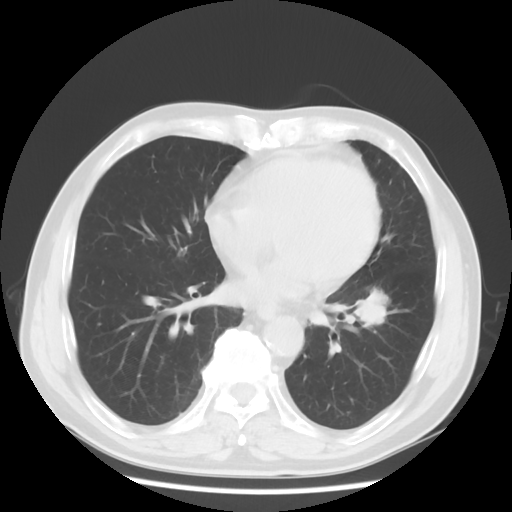
Chest CT, one axial slice. Slice 27 of 68 in the series (ordered by position). Lung window (W 1500 / L -600 HU). 5 mm slice thickness. 512 × 512 image matrix. Male patient, age 71 years. From the clinical record (not read from this slice): clinical TNM (as recorded): T1c N1 M0.
Annotated regions visible in this slice (rectangle marked by the reading radiologist):
- lung tumour (recorded histology: adenocarcinoma): bounding box [x1, y1, x2, y2] px = [353, 278, 399, 341]